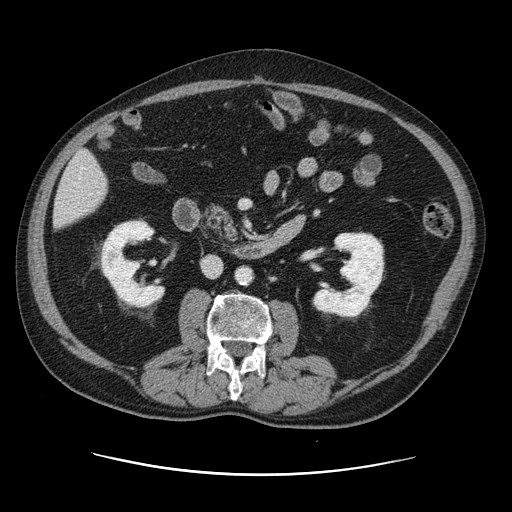
Contrast-enhanced abdominal CT, one axial slice; position 37 of 141 along the scan axis; 120 kVp; soft-tissue window (W 400 / L 40 HU); 512 × 512 image matrix, field of view 395 × 395 mm. Male patient, age 72 years. Case-level facts recorded for this patient, not image findings: diagnosis: colorectal cancer liver metastases, imaged before liver resection.
Annotated regions visible in this slice (manually delineated by an expert):
- liver: bounding box <54,151,108,228> (left, top, right, bottom; pixels)
- planned liver remnant (the part of the liver to remain after resection): <54,151,108,228>